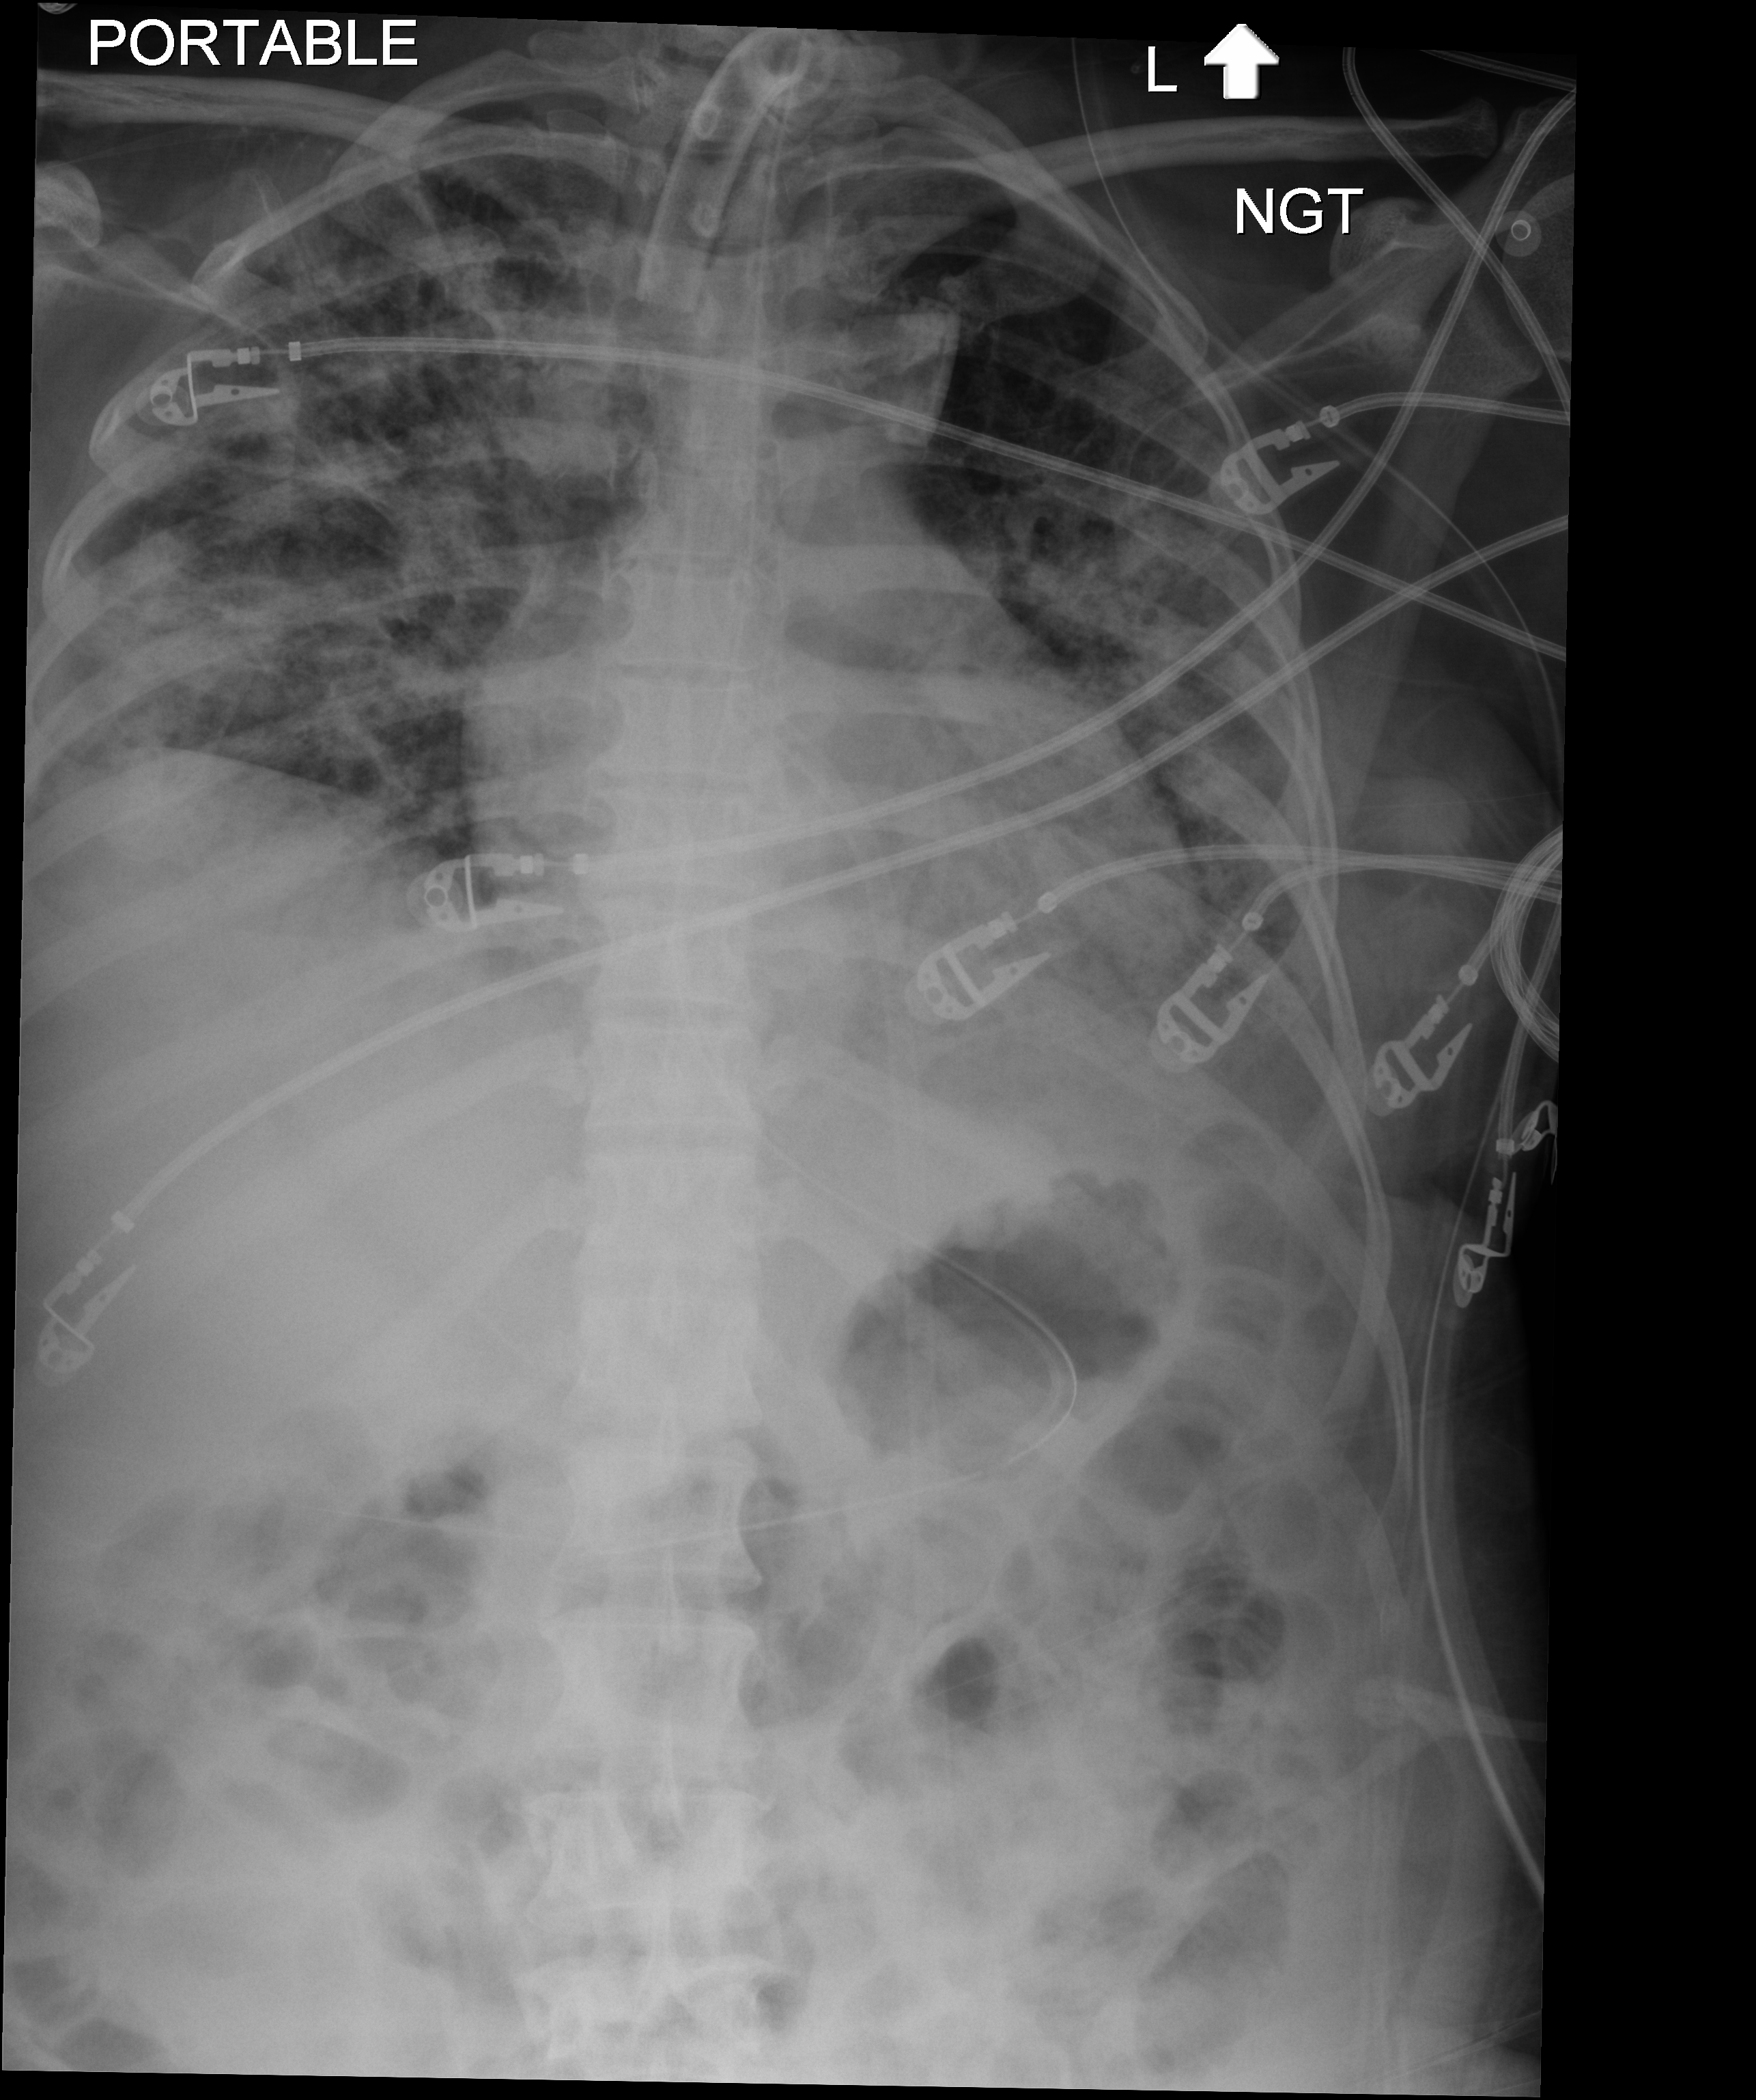
Bedside chest radiograph (digital radiography); anteroposterior (AP) projection. Female patient hospitalised with COVID-19, age 18–59 years.
Hospital-stay facts (about this admission, not read from this image; timing relative to this image not recorded):
- hypertension (admission record): no
- mechanically ventilated during this hospital stay: yes